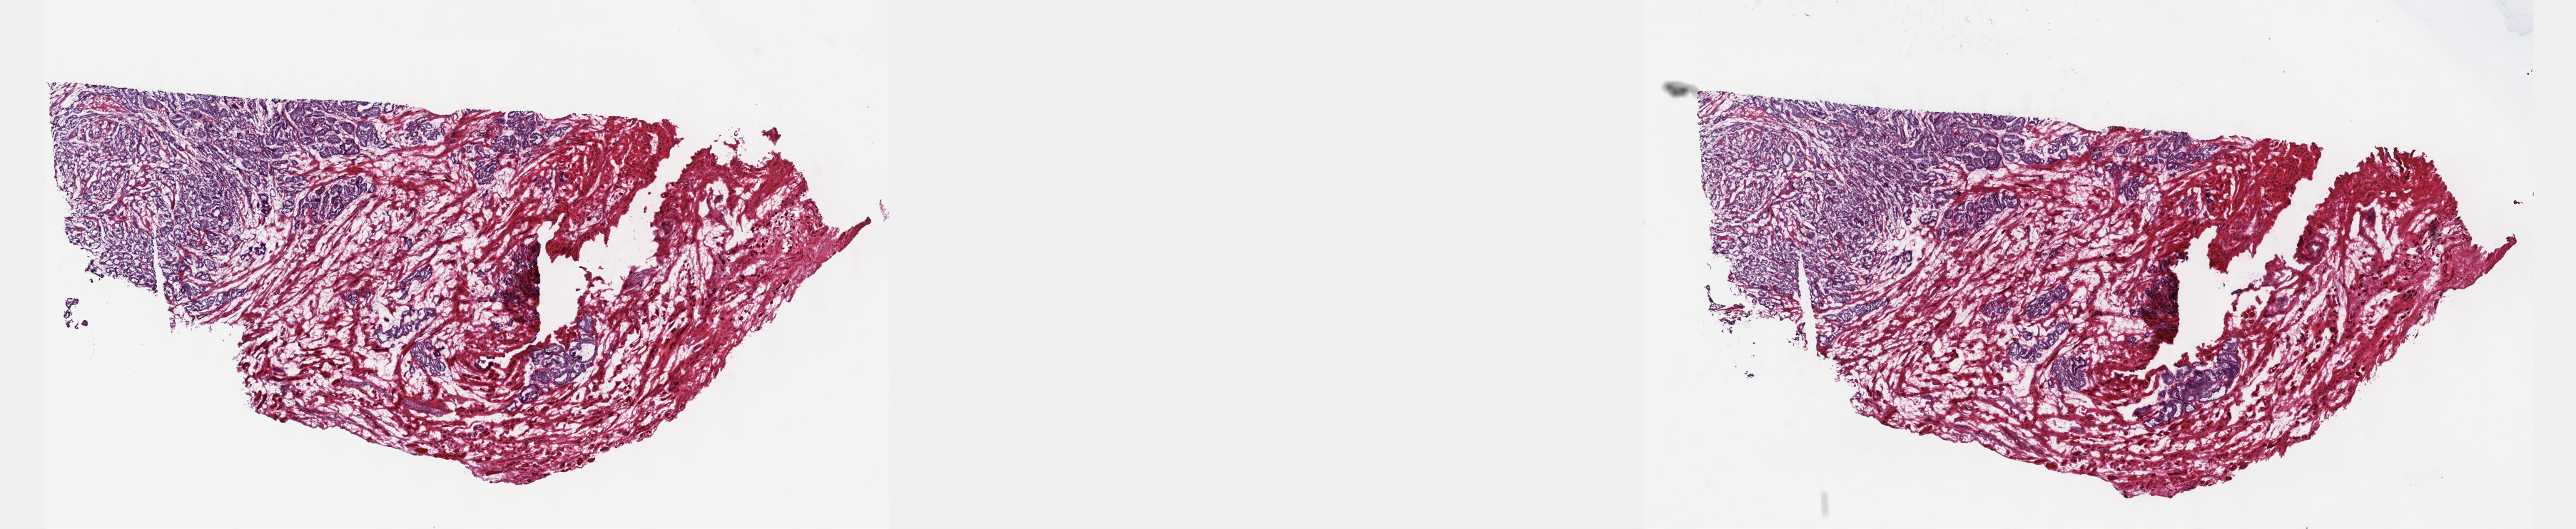
Whole-slide histology image, H&E, shown as a low-resolution overview of the whole scanned area (about 29.2 x 6.0 mm), frozen section from the top of the tissue portion, sample: primary tumour, prostate. Male, age 58 years at initial diagnosis. Gleason score: 7 (3+4). Pathologist review of this section (percent, as recorded): tumour cells 50%, tumour nuclei 60%, normal cells 50%, stromal cells 0%, necrosis 0%. Inflammatory infiltration, as recorded: lymphocyte infiltration 0%, monocyte infiltration 0%, neutrophil infiltration 0%.
Diagnosis: Adenocarcinoma, NOS (prostate gland).